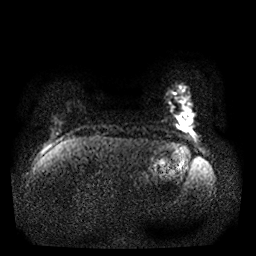
Breast MRI, one axial slice. Position 2 of 25 along the scan axis. Diffusion-weighted series; image 2 of 4 stored at this slice position (different b-values; order by instance number). 1.5 T. 256 × 256 image matrix. Female patient.
Annotated regions visible in this slice (outlined manually by an expert reader):
- tumour on diffusion-weighted imaging: bounding box (x1, y1, x2, y2) in pixels: (174, 113, 196, 133)